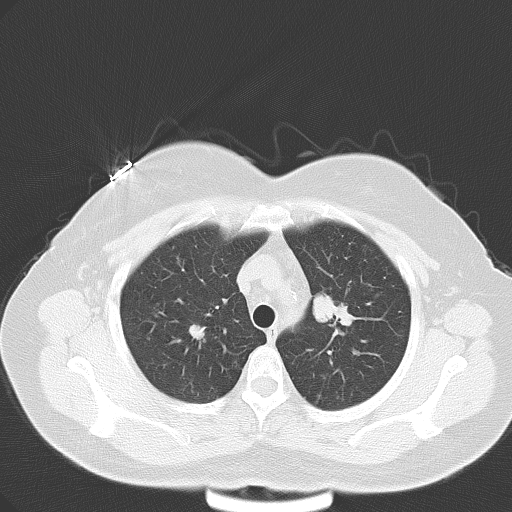
Chest CT, one axial slice; slice 43 of 57 in the series (ordered by position); reconstruction kernel B70f; 120 kVp; lung window (W 1500 / L -600 HU); 5 mm slice thickness; 512 × 512 image matrix, field of view 353 × 353 mm. Female patient, age 53 years. Case-level facts recorded for this patient, not image findings: clinical TNM (as recorded): T1c N0 M1a.
Structures marked on this image (bounding box drawn by a radiologist):
- lung tumour (recorded histology: adenocarcinoma): box from (x=313, y=293) to (x=357, y=329) px